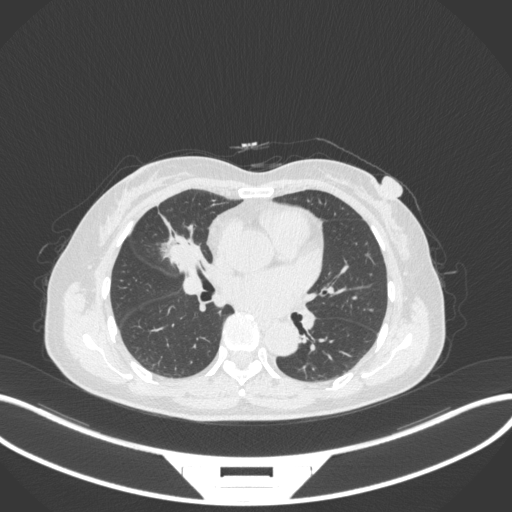
Chest CT, one axial slice; slice 154 of 282 in the series (ordered by position); 120 kVp; lung window (W 1500 / L -600 HU); 1 mm slice thickness; 512 × 512 image matrix, field of view 400 × 400 mm. Patient: female, 51 years. From the clinical record (not read from this slice): clinical TNM (as recorded): T1c N0 M0.
Annotated regions visible in this slice (bounding box drawn by a radiologist):
- lung tumour (recorded histology: adenocarcinoma): bounding box (x1, y1, x2, y2) in pixels: (154, 225, 210, 276)